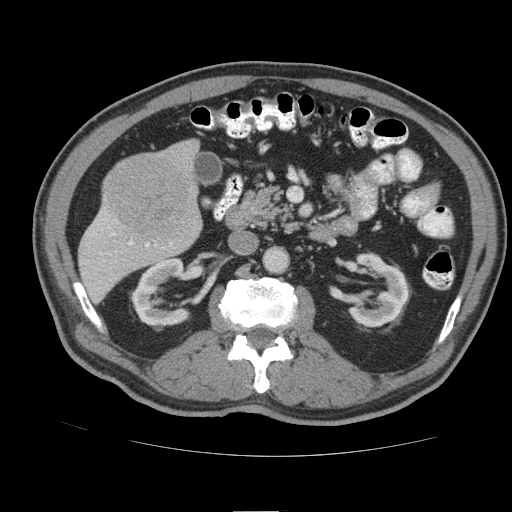
Contrast-enhanced abdominal CT (liver protocol), one axial slice; position 34 of 105 along the scan axis; reconstruction kernel STANDARD; 140 kVp; soft-tissue window (W 400 / L 40 HU); 2.5 mm slice thickness; 512 × 512 image matrix, field of view 380 × 380 mm. From the clinical record (not read from this slice): diagnosis: hepatocellular carcinoma (patient treated with transarterial chemoembolisation; whether this scan precedes or follows treatment is not stated here); TNM stage (as recorded): Stage-IIIB; Child-Pugh class: A.
Annotated regions visible in this slice (semi-automatically segmented with operator editing):
- liver parenchyma outside the tumour (the mass and vessels are separate outlines, so this box may not span the whole liver): bounding box (x1, y1, x2, y2) in pixels: (78, 140, 202, 302)
- mass: (104, 155, 197, 239)
- liver vessels: (109, 227, 172, 247)